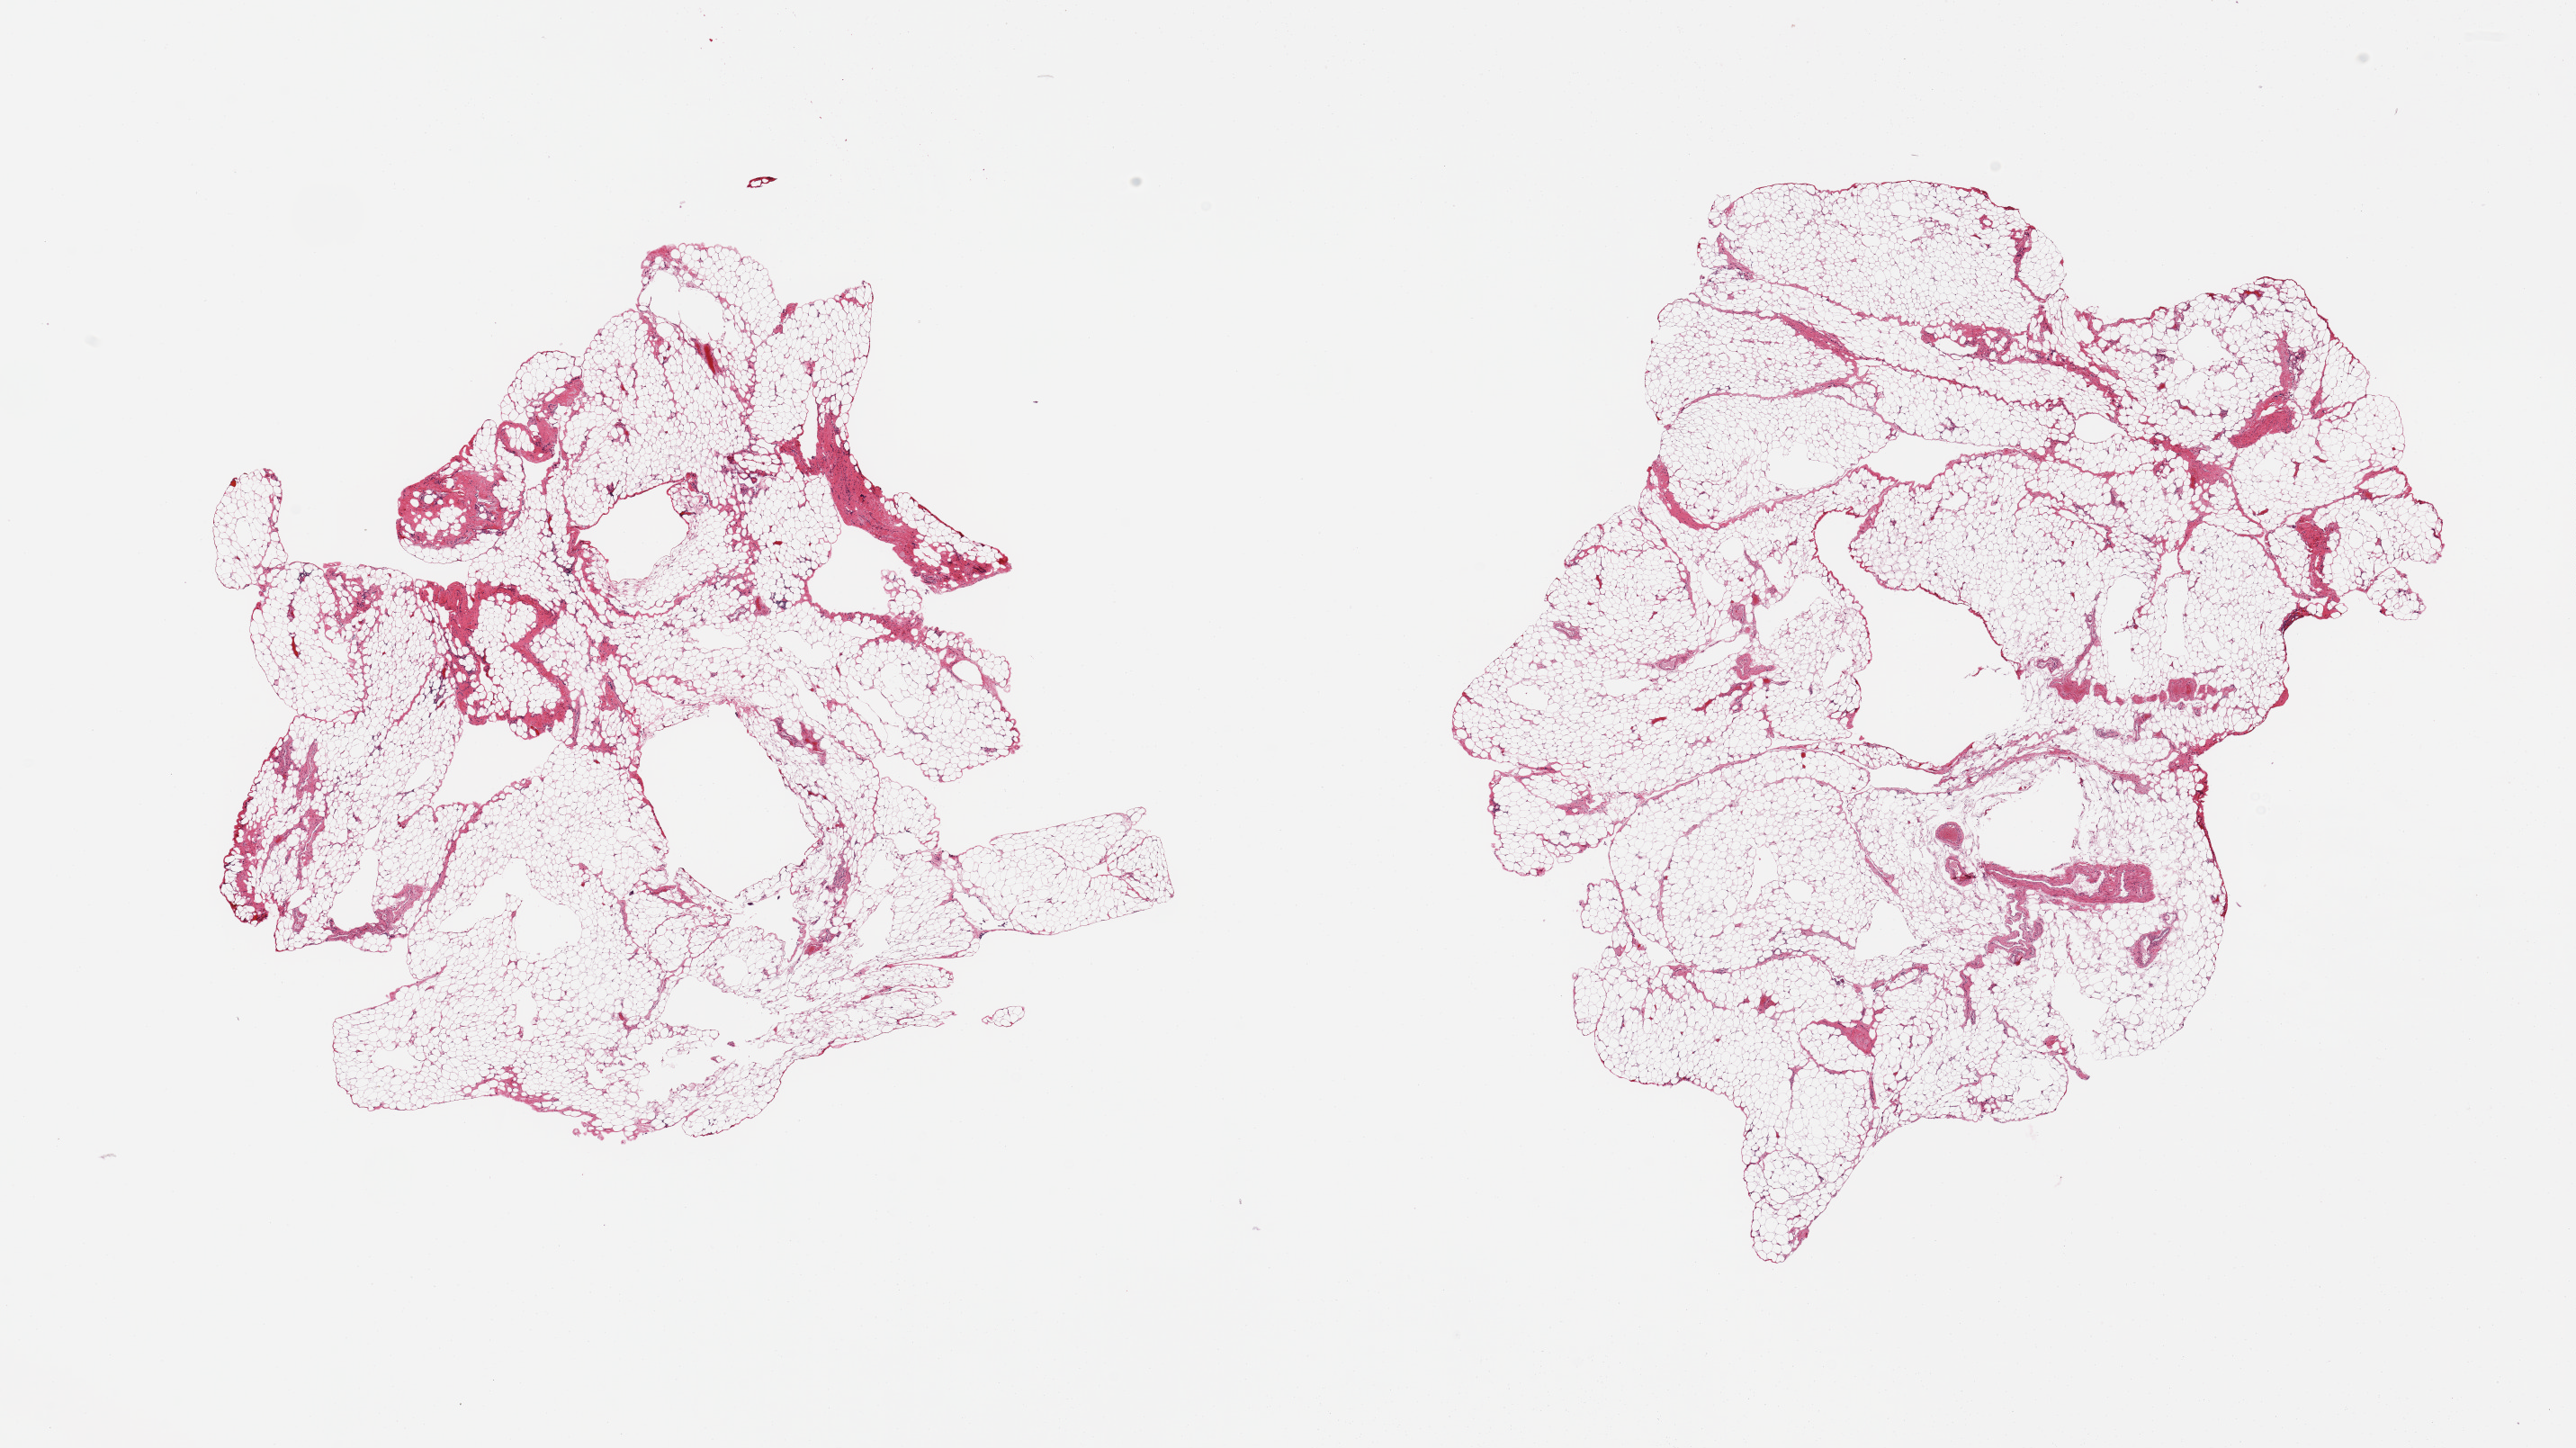
Digitized H&E-stained section, brightfield, a low-resolution overview of the entire scanned area, about 22.6 x 12.7 mm (from a 20x scan). PAXgene-fixed, paraffin-embedded tissue. Sampled site (target tissue): omentum. Tissue donor sample. Male donor.
Reviewer comment on this tissue sample: 2 pieces; 10% fibrous content.